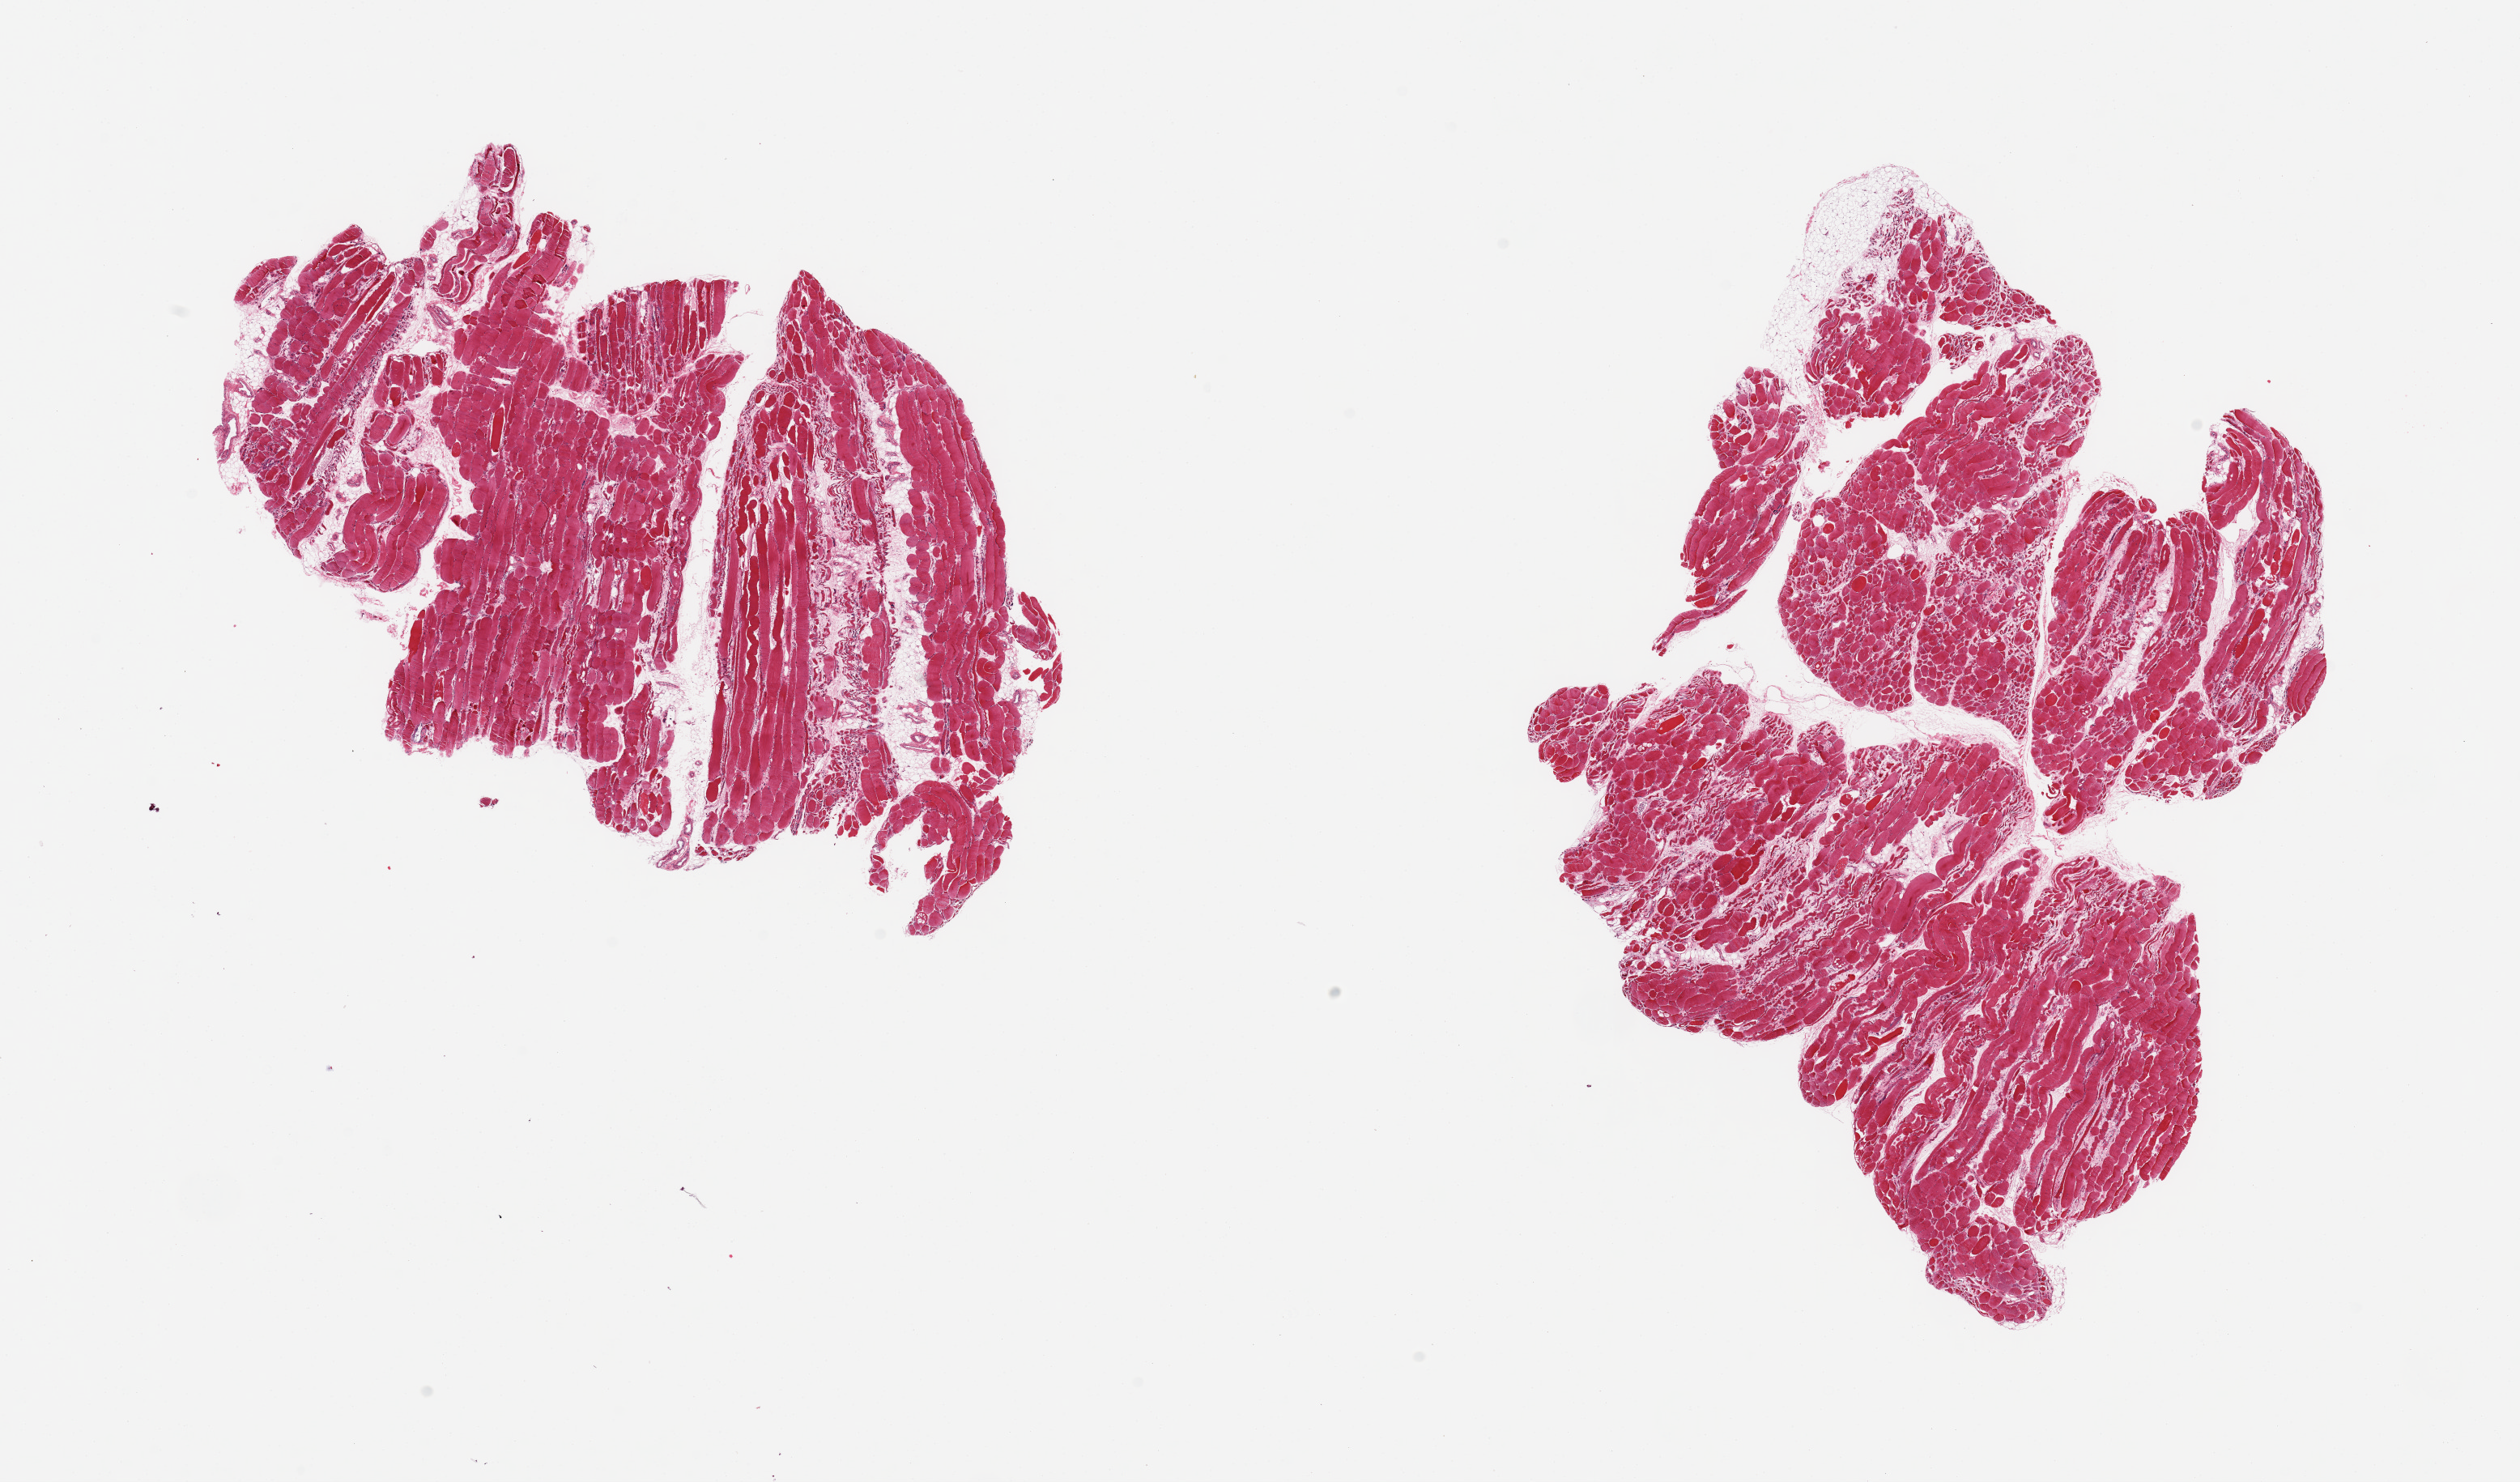
Whole-slide image, haematoxylin and eosin stain, brightfield, whole scanned area (about 24.6 x 14.5 mm) shown as a low-resolution overview; PAXgene-fixed paraffin-embedded (PFPE) section; section of skeletal muscle (target tissue); donor tissue sample.
Reviewer comment on this tissue sample: 2 pieces, ~15% interstitial fat; Many fibres appear atrophic and/or degenerated.